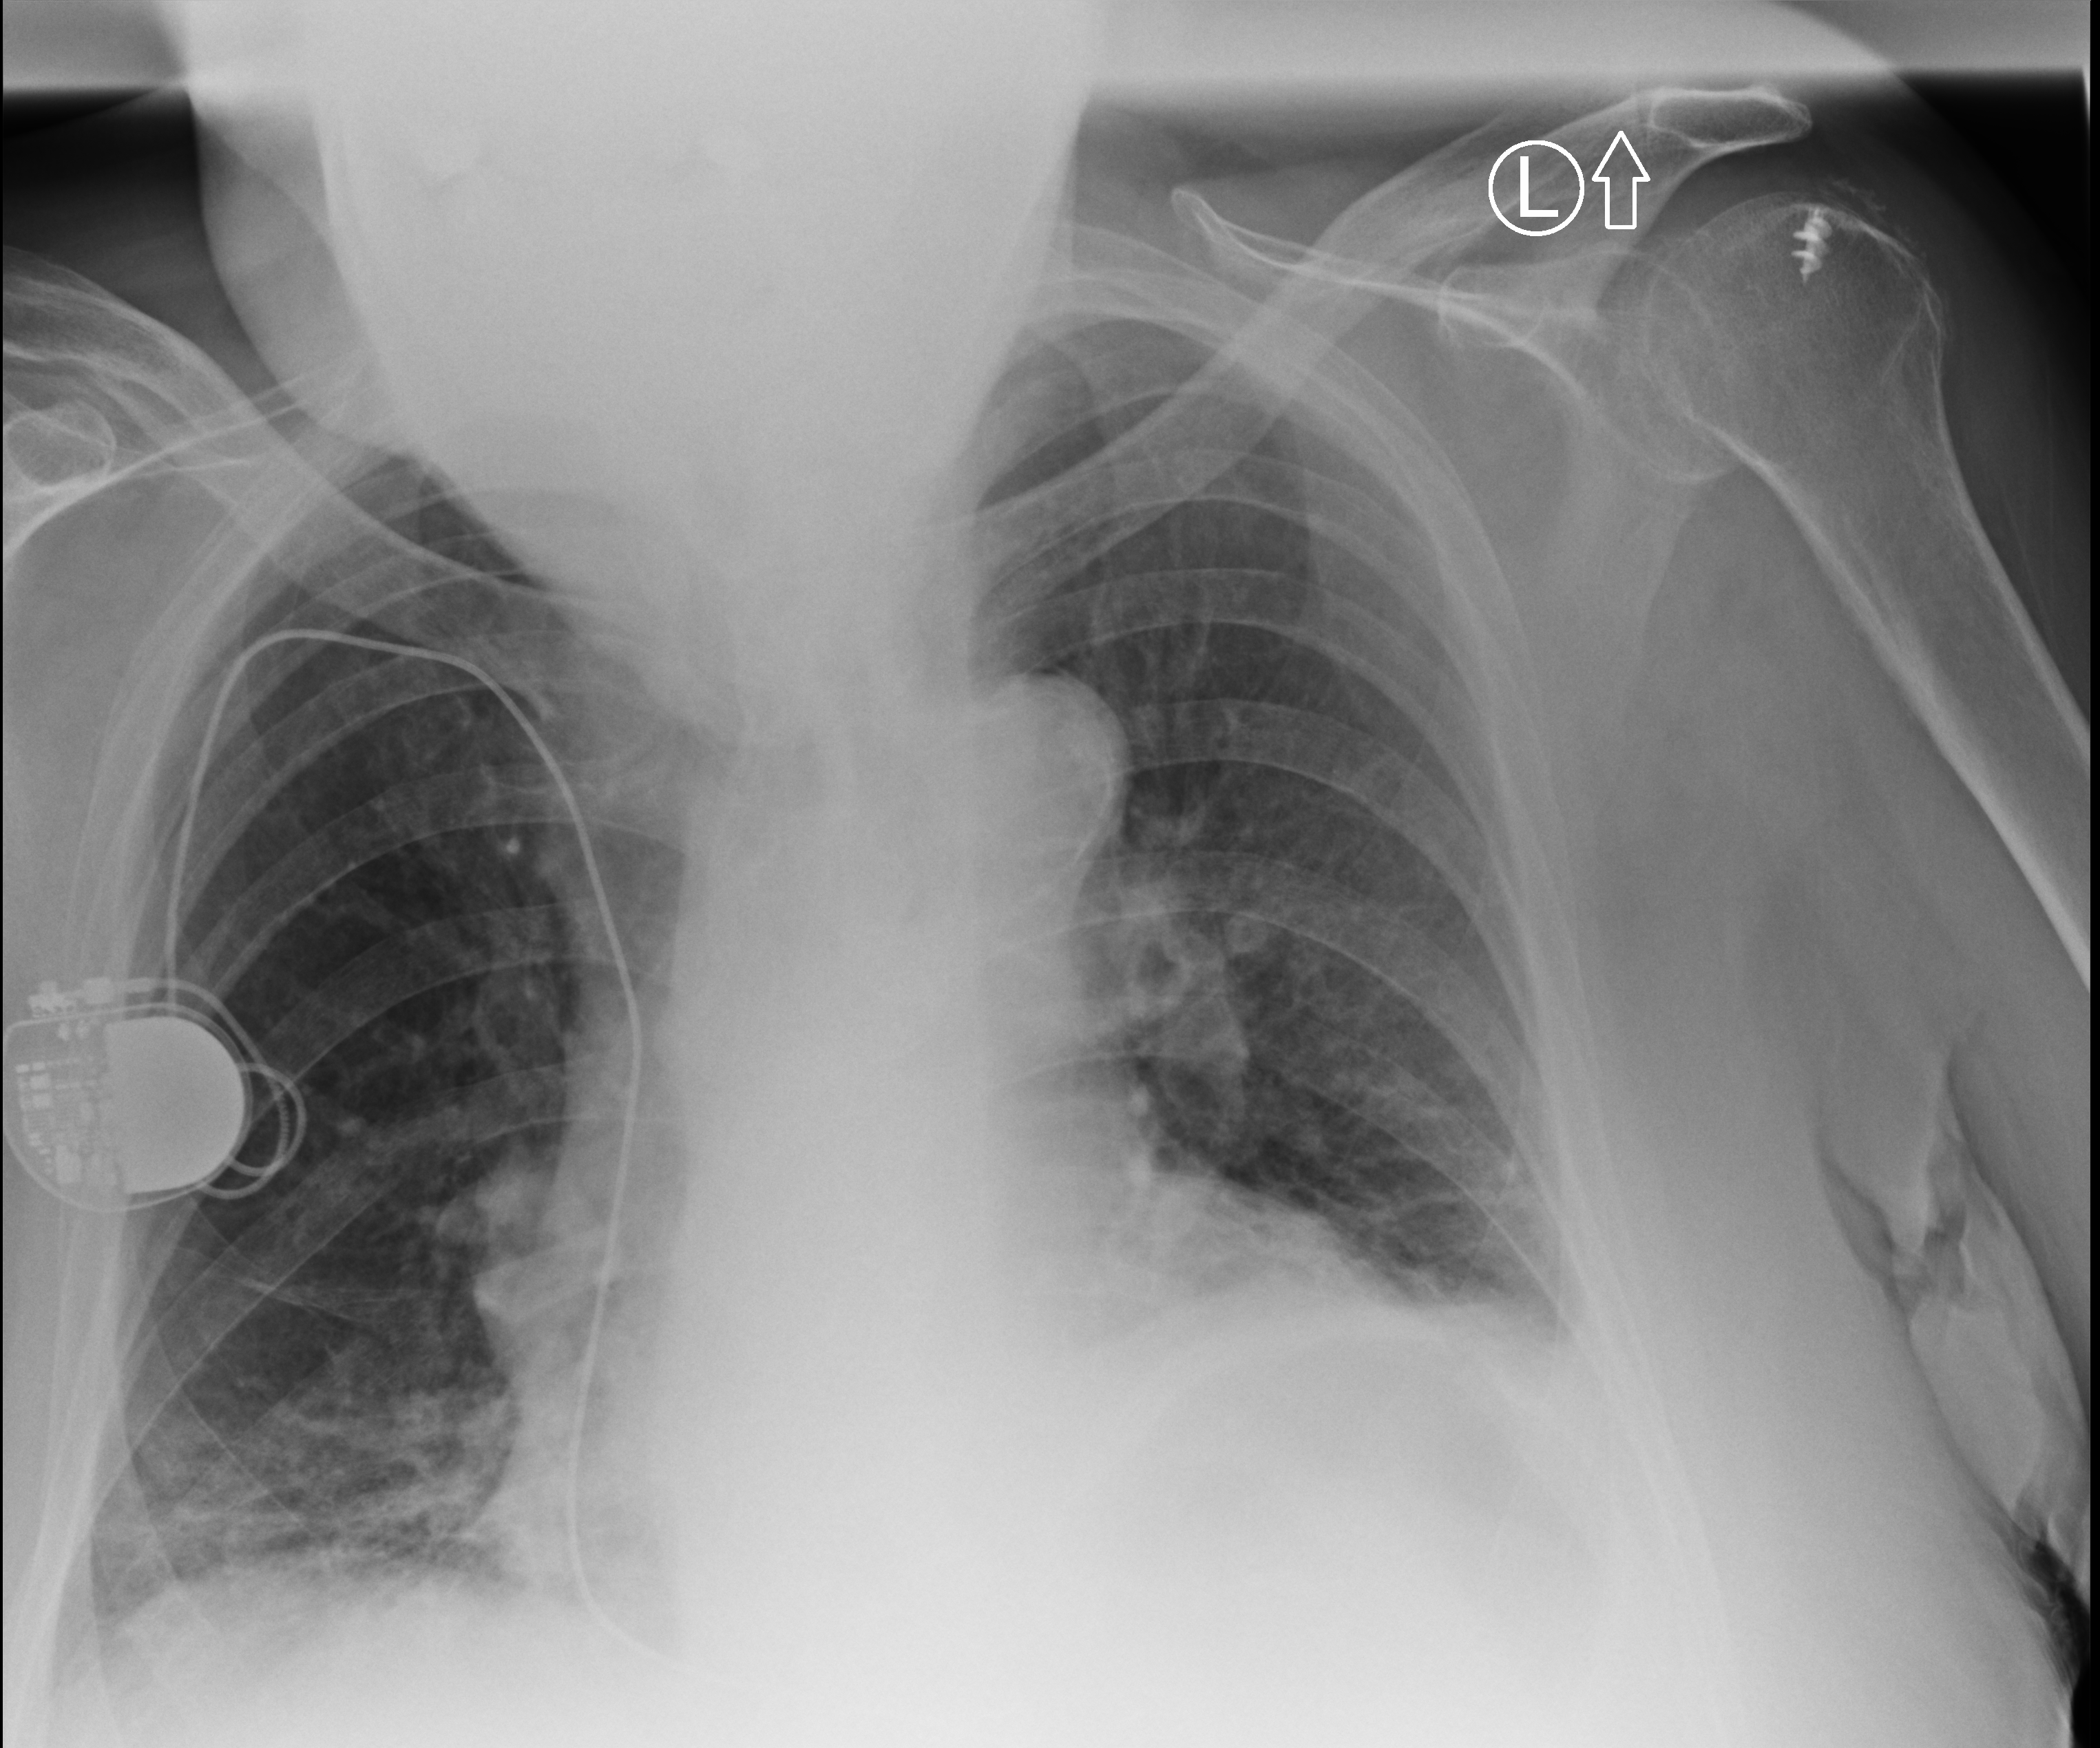
Bedside chest radiograph (computed radiography), anteroposterior (AP) projection. Male patient hospitalised with COVID-19, age 75–90 years.
Hospital-stay facts (about this admission, not read from this image; timing relative to this image not recorded): length of hospital stay: 5 days.